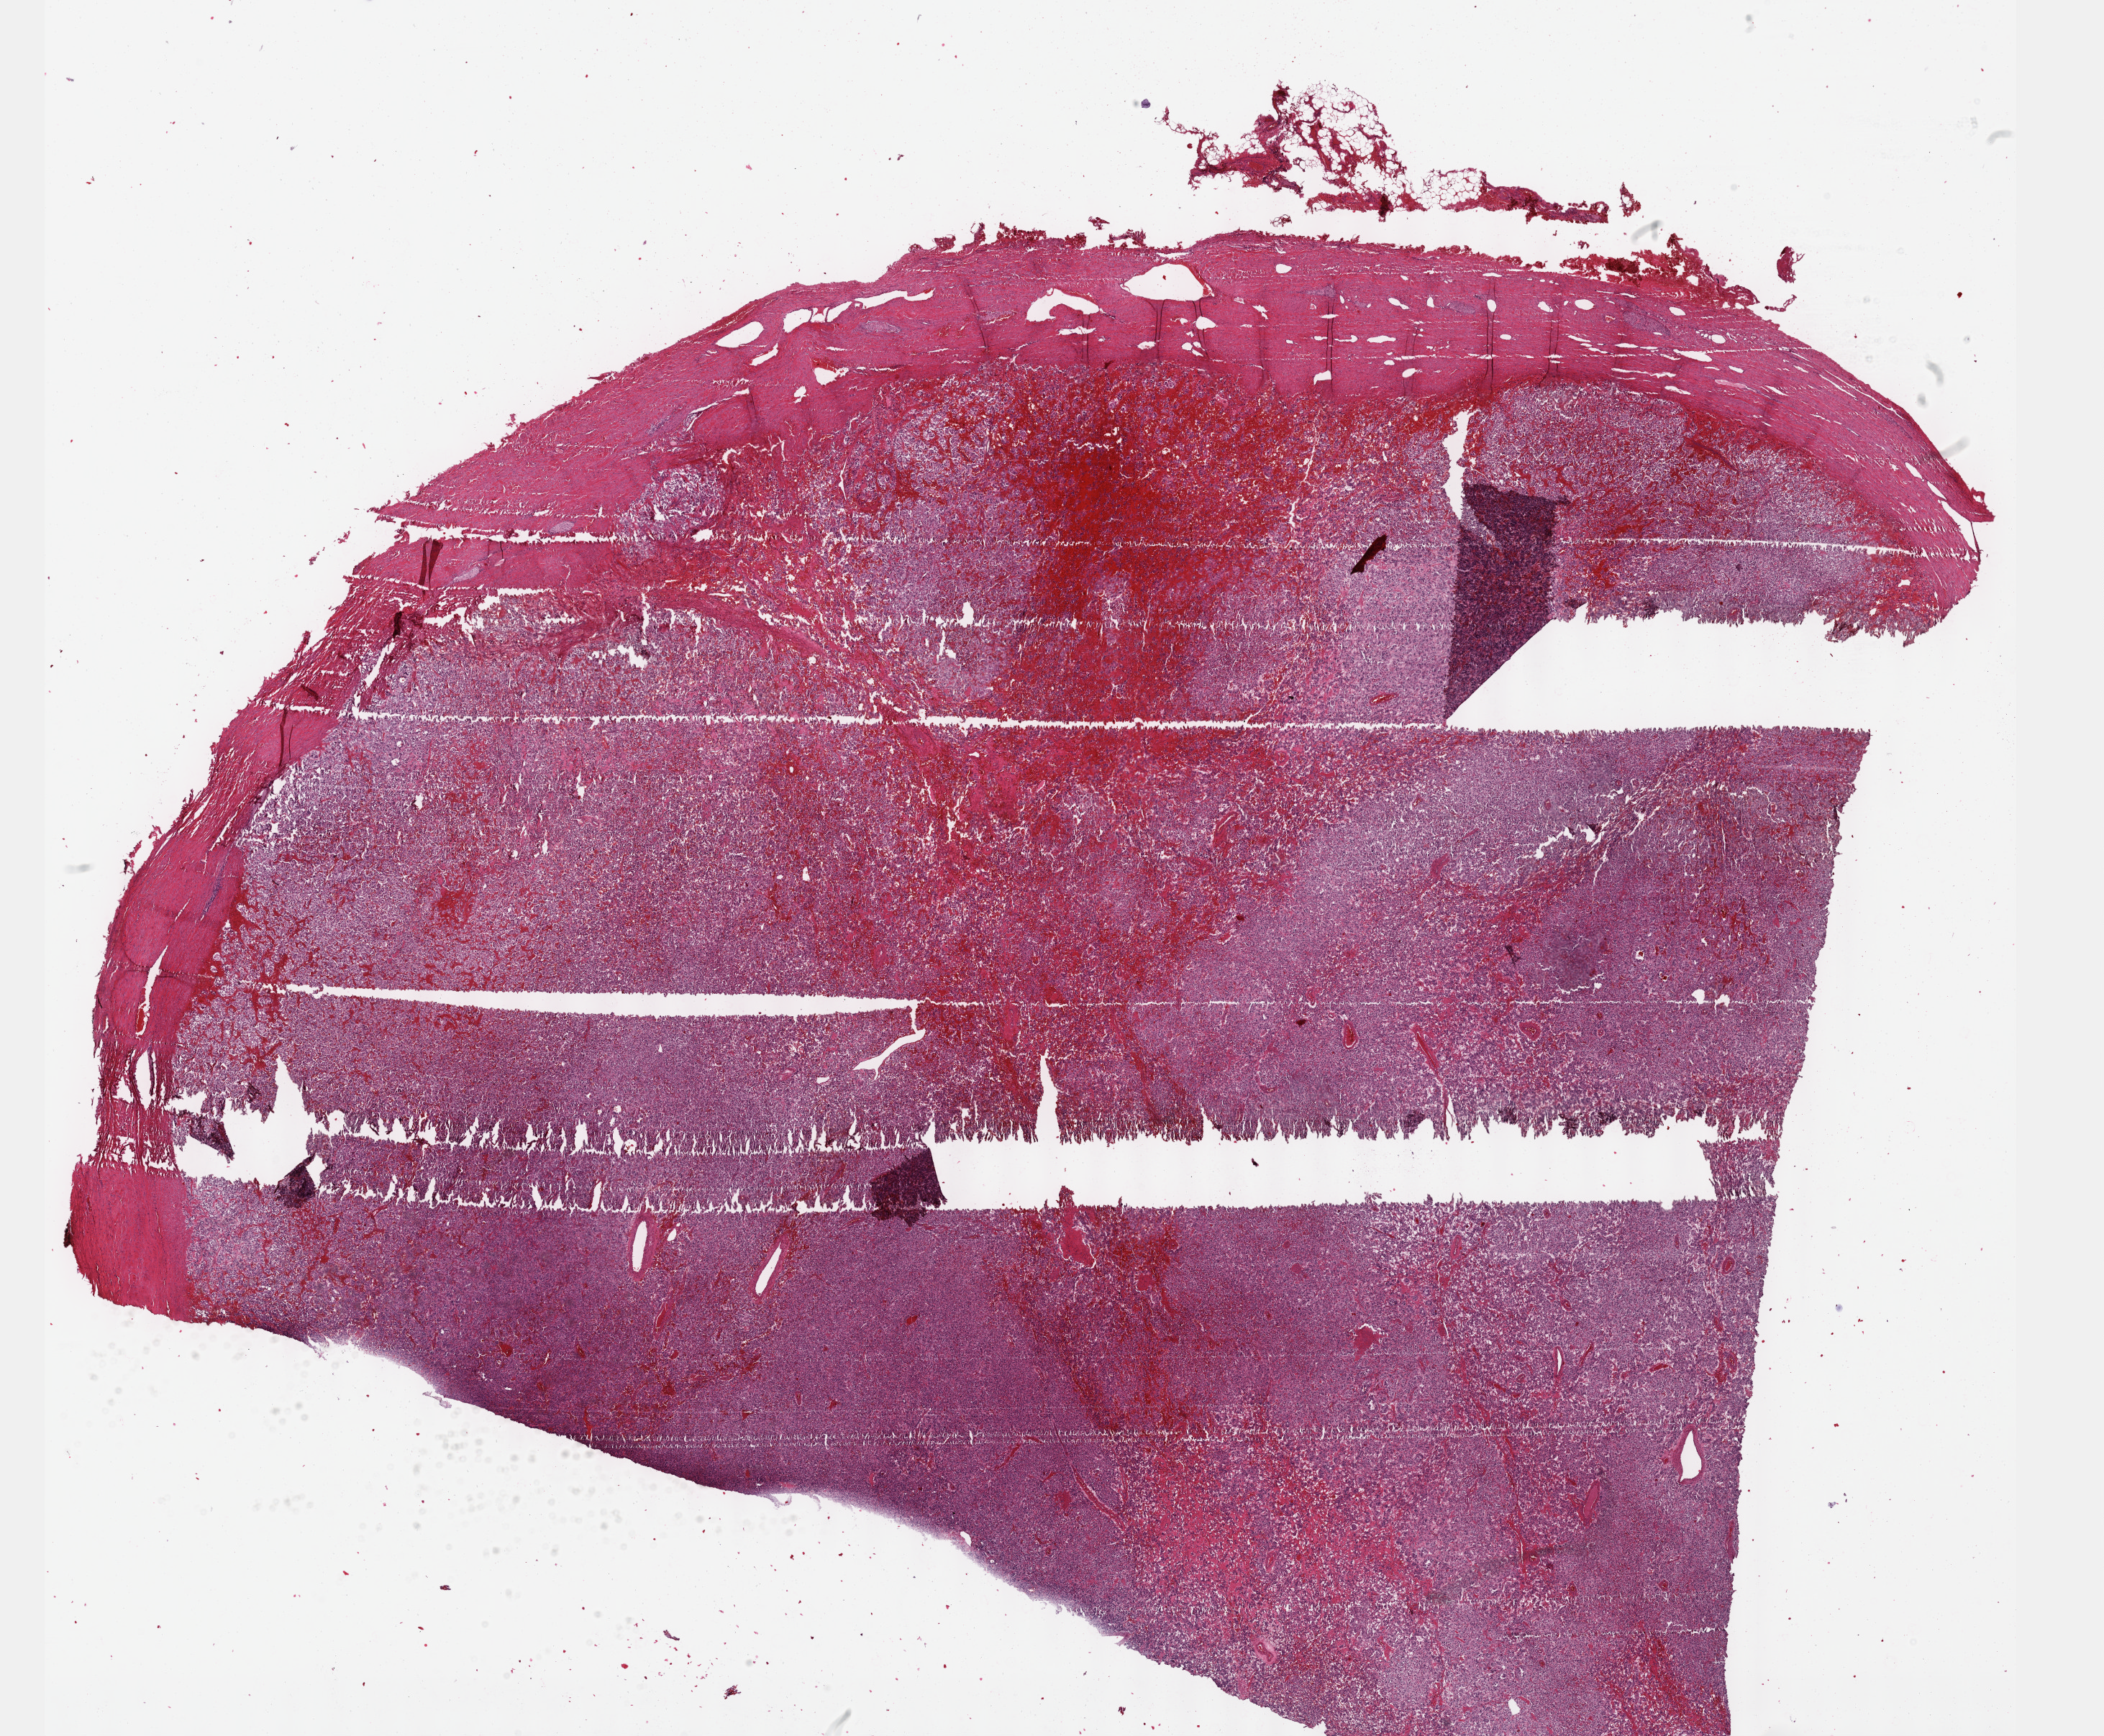
Whole-slide histology image, H&E-stained, shown as a low-resolution overview of the whole scanned area (about 23.6 x 19.5 mm, slide scanned at 40x), formalin-fixed paraffin-embedded (FFPE) diagnostic section, sample: primary tumour, retroperitoneum and peritoneum. Female, age 35 years at initial diagnosis.
Histologic diagnosis: Extra-adrenal paraganglioma, malignant (retroperitoneum).